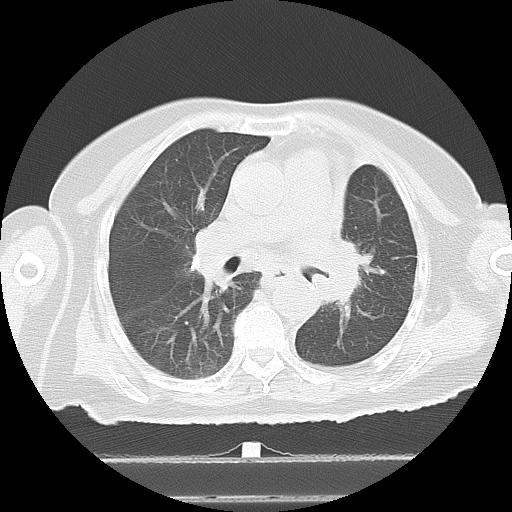
Chest CT, one axial slice. Slice 9 of 27 in the series (ordered by position). 120 kVp. Lung window (W 1500 / L -600 HU). 5 mm slice thickness. 512 × 512 image matrix, field of view 350 × 350 mm. Patient: female, 67 years. From the clinical record (not read from this slice): clinical TNM (as recorded): T1a N1 M1c; histopathological grade: G2.
Outlined on this slice (bounding box drawn by a radiologist):
- lung tumour (recorded histology: adenocarcinoma): bounding box (x1, y1, x2, y2) in pixels: (319, 228, 372, 312)